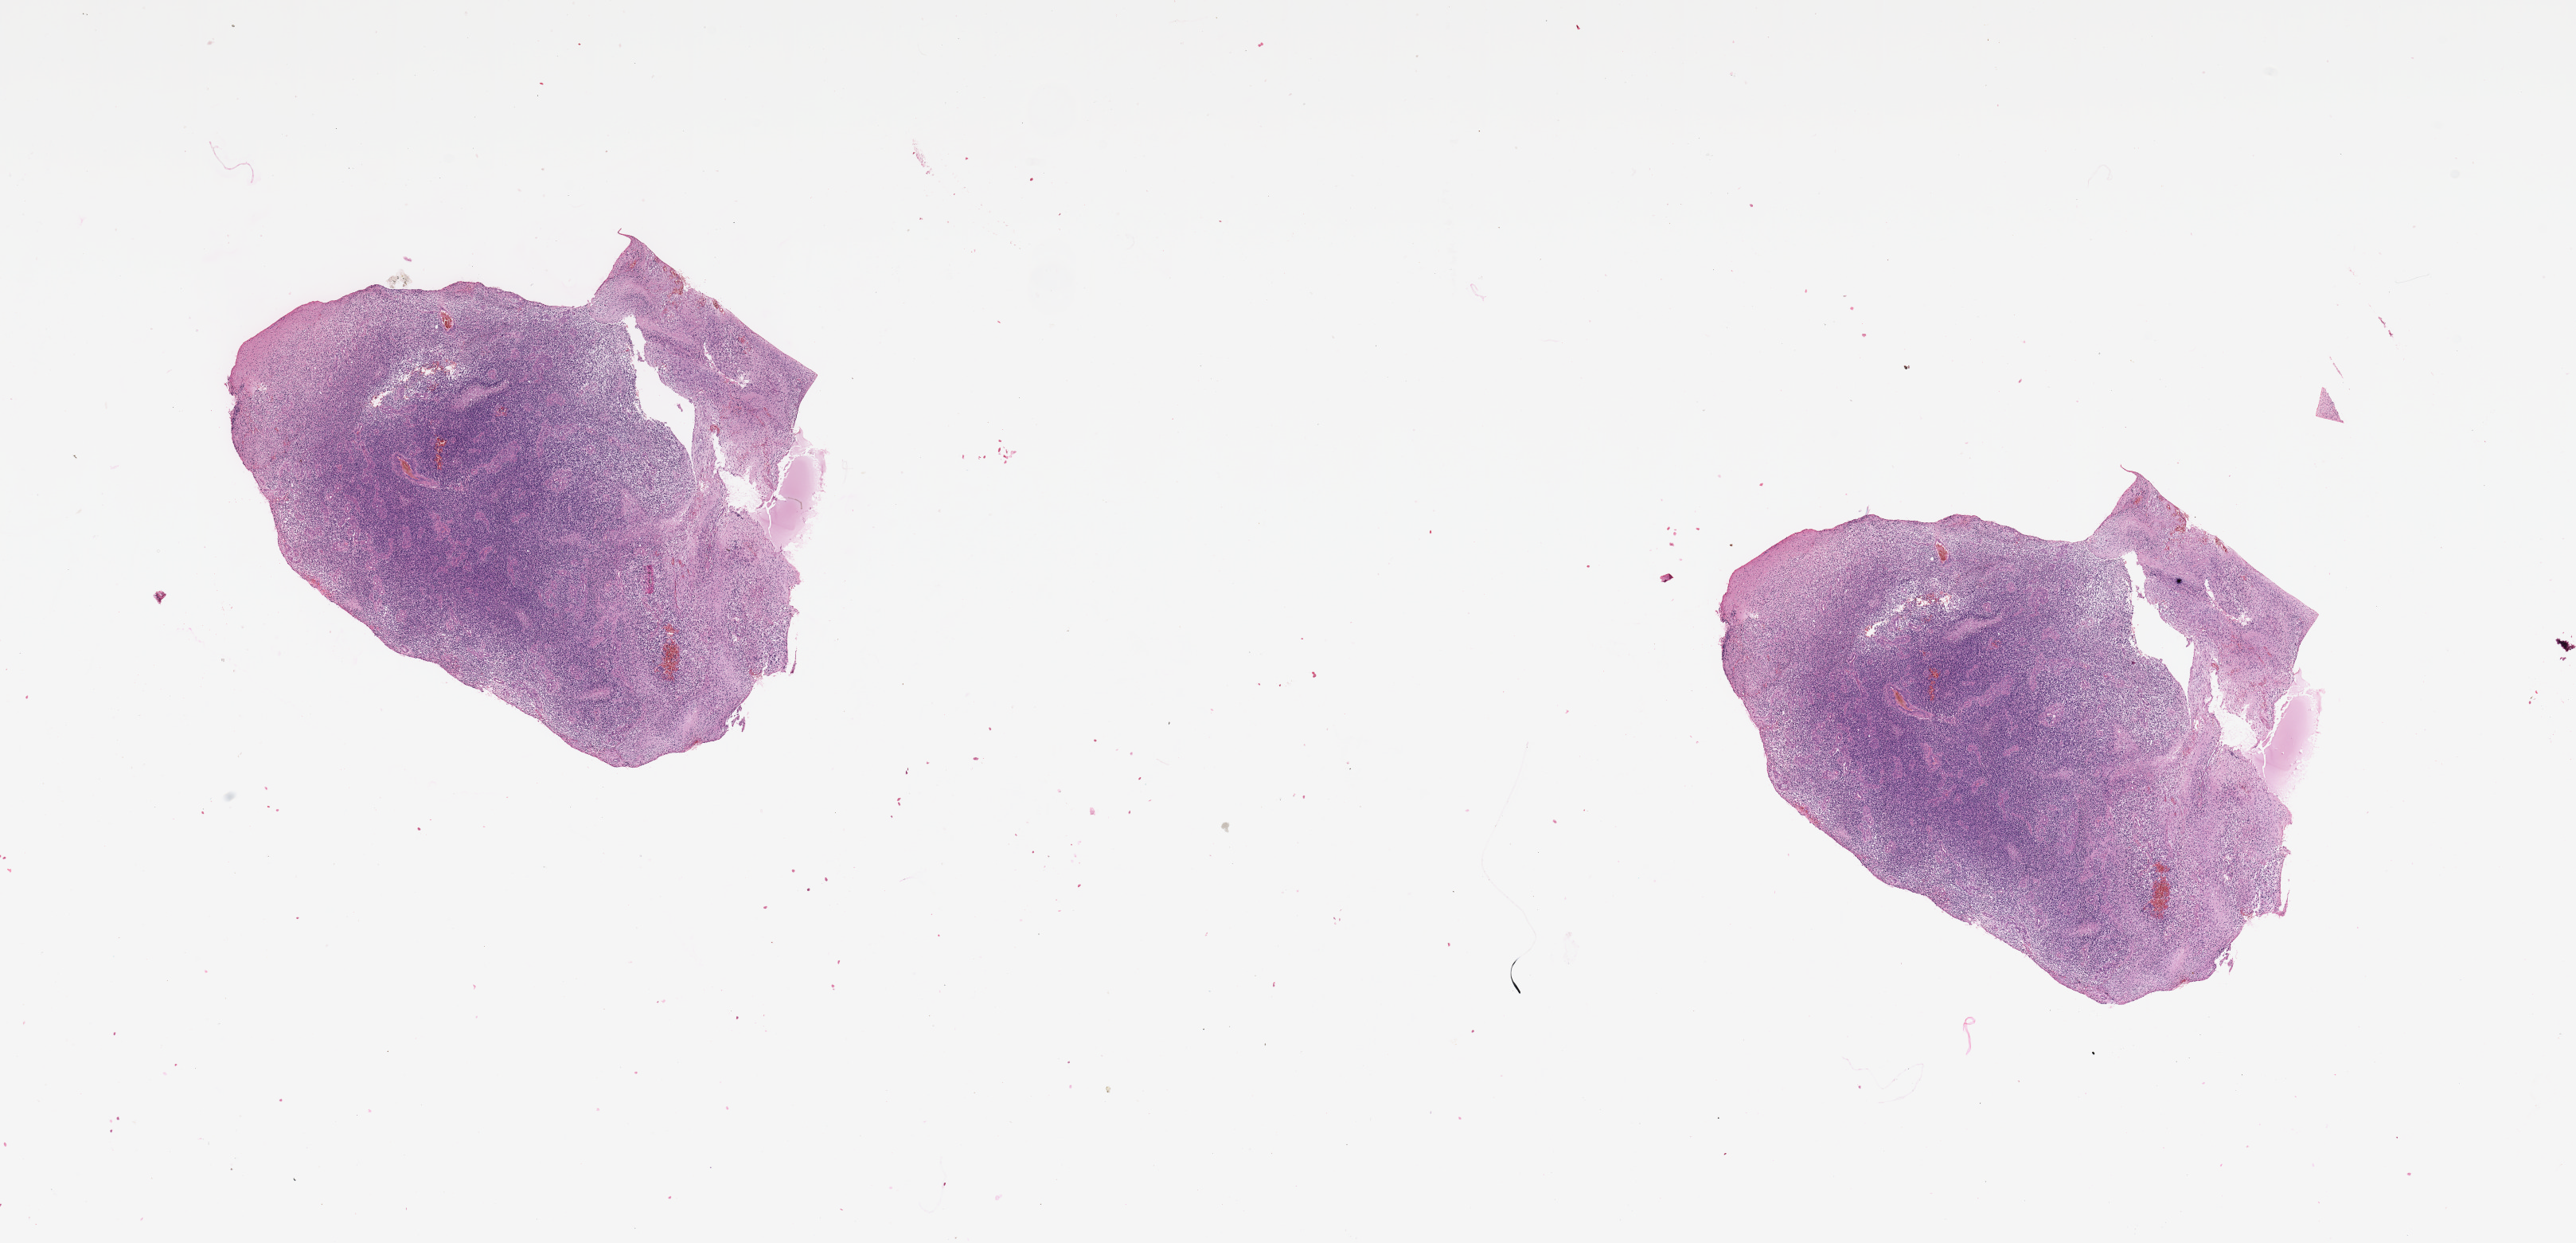
Whole-slide histology image, H&E, low-resolution overview of the scanned area, about 25.6 x 12.3 mm (slide scanned at 20x). Tumour tissue sample, sampled site: brain. Female, 68 y/o. Pathologist review of this section (percent, as recorded): tumour nuclei 80%, necrosis 10%.
- diagnosis: Glioblastoma
- primary tumour site (as recorded): parietal lobe